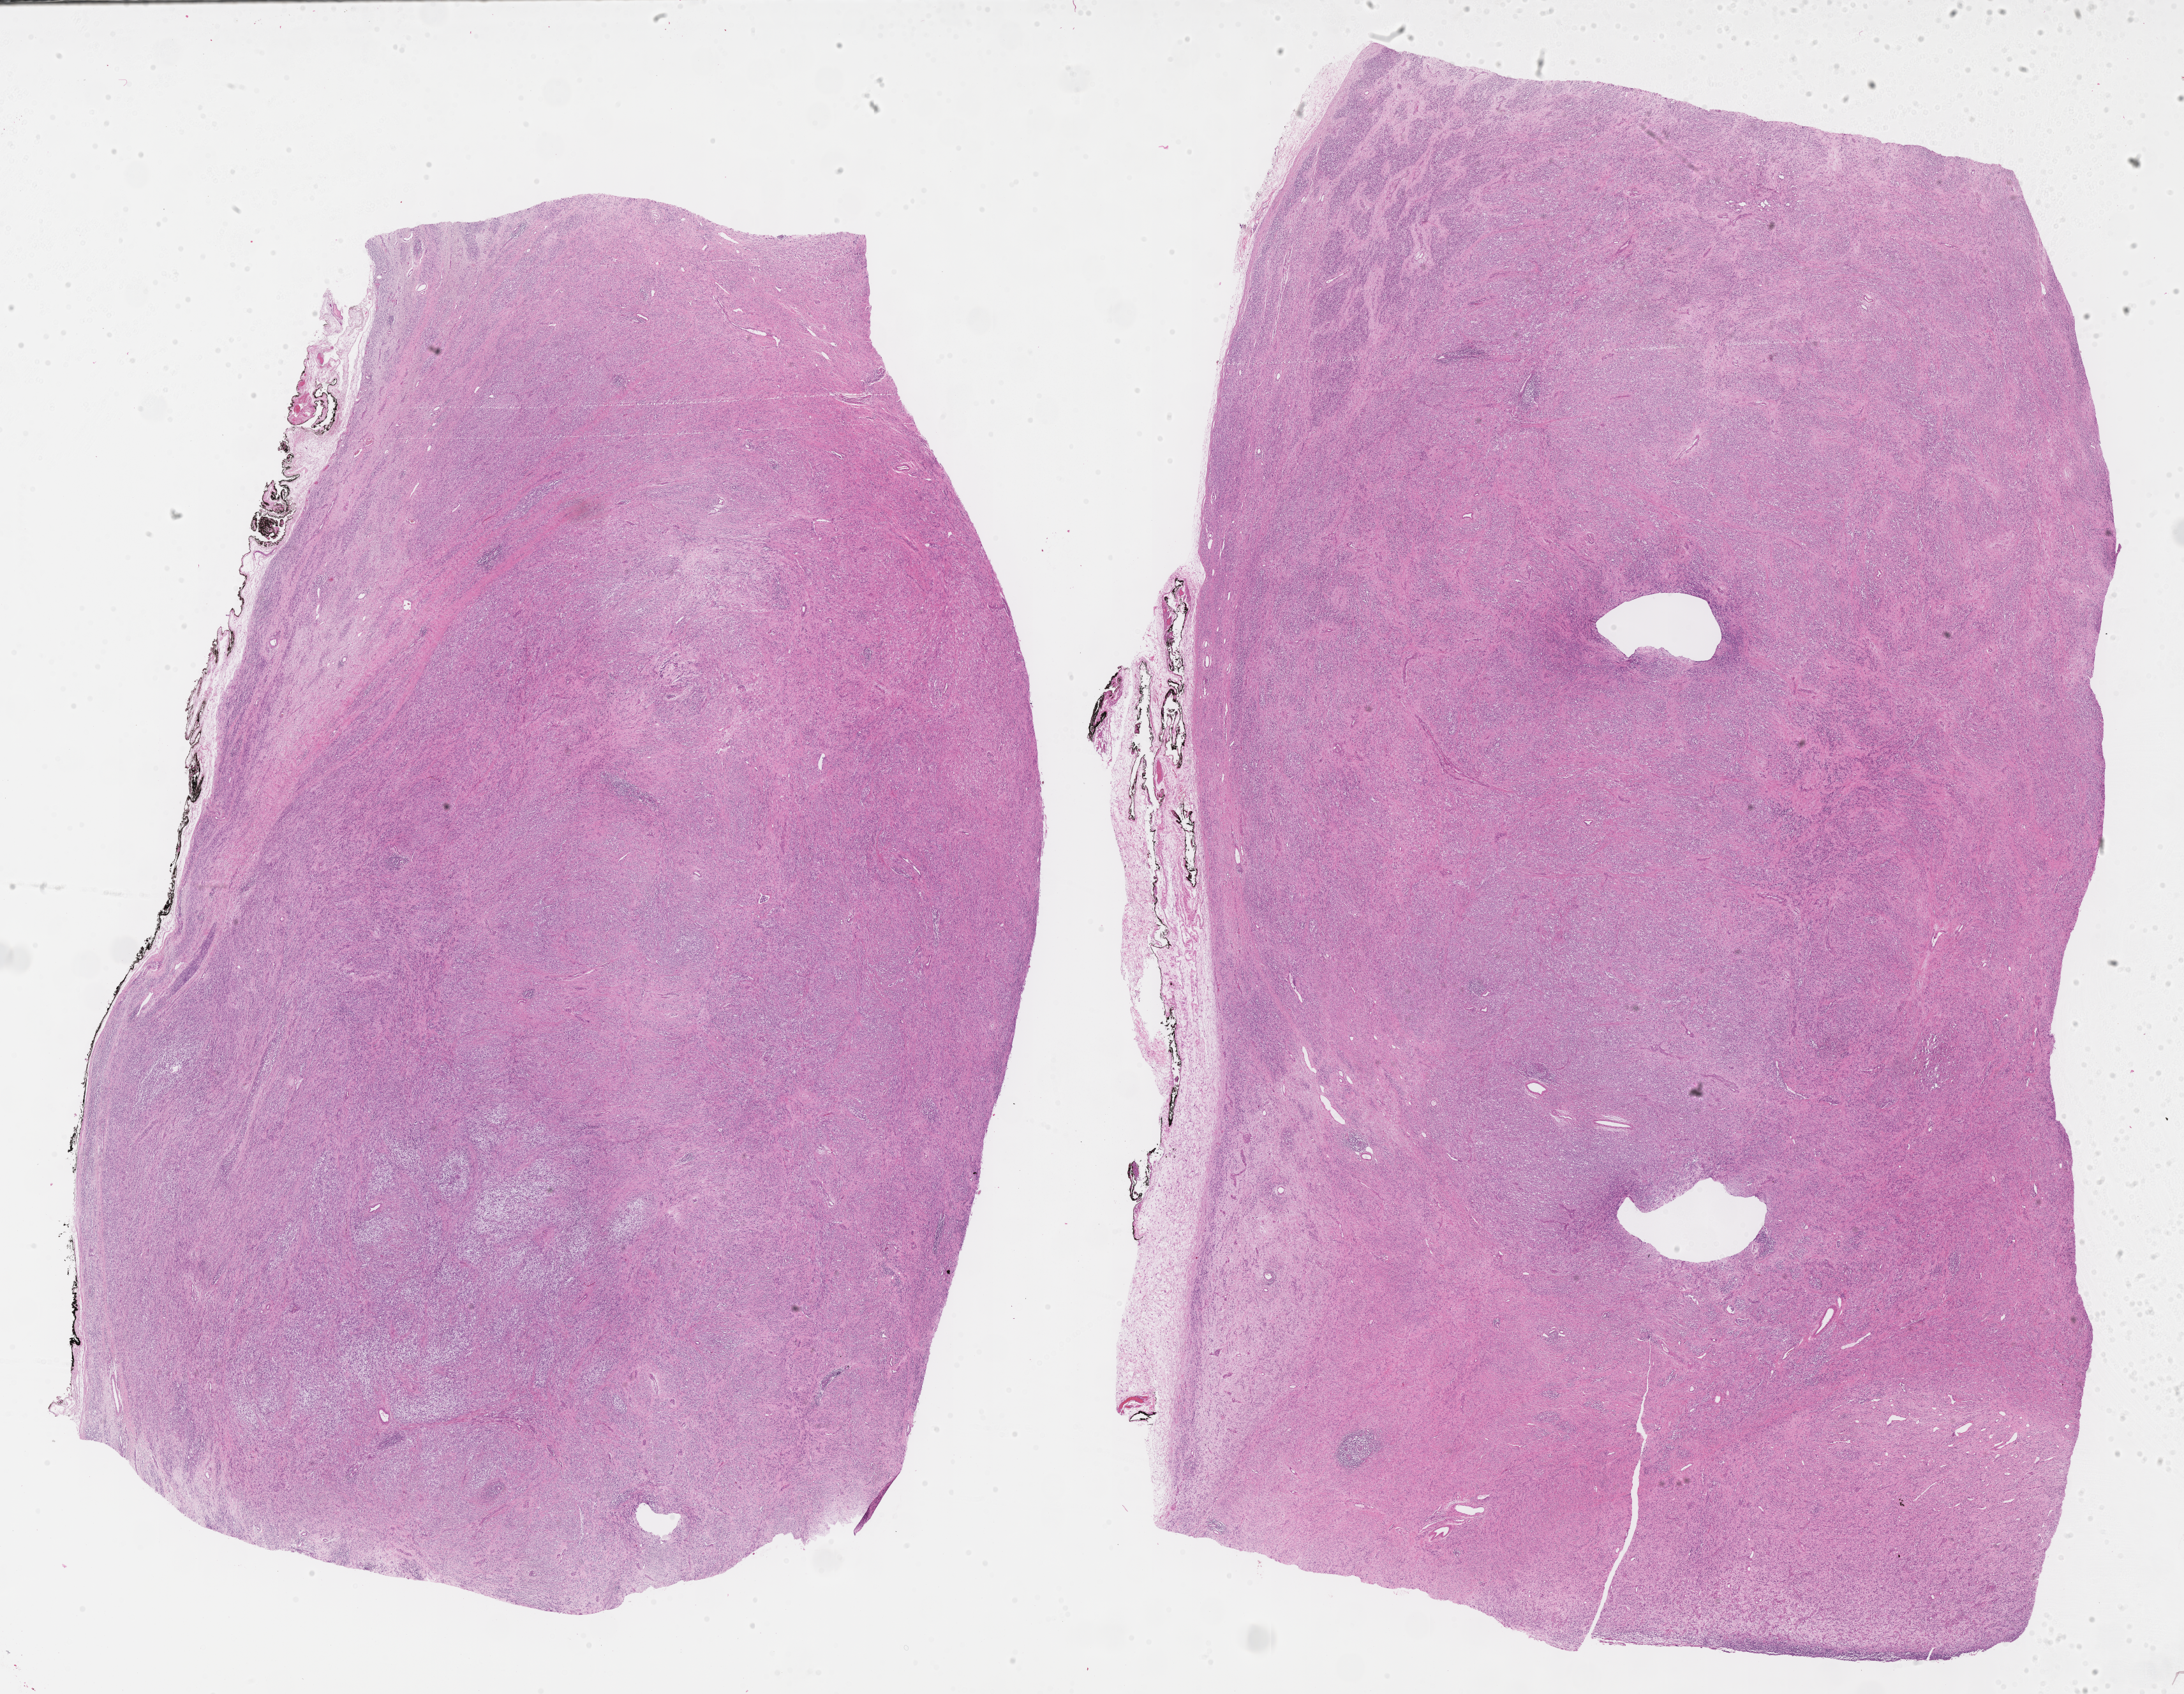
Digitized hematoxylin and eosin (H&E)-stained section of tumor tissue, a low-resolution overview of the entire scanned area, about 27.7 x 21.5 mm; formalin-fixed, paraffin-embedded (FFPE) tissue; sample anatomic site: testicle, left. Male patient, age at diagnosis 4.5 years.
Stage (as recorded): 1. Metastatic status at presentation (as recorded): non-metastatic. Diagnosis: rhabdomyosarcoma; histological classification: embryonal rhabdomyosarcoma.